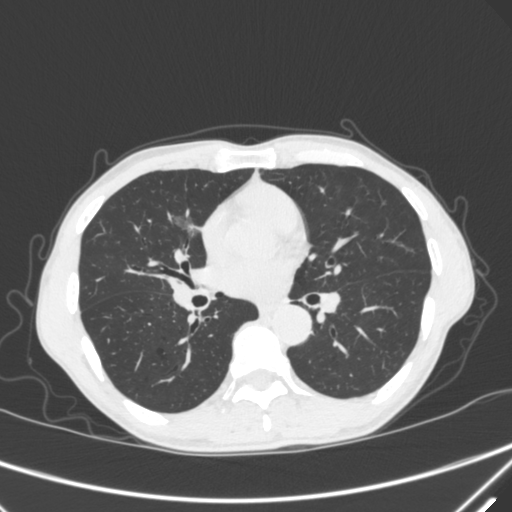
Chest CT, one axial slice; position 172 of 340 along the scan axis; 120 kVp; lung window (W 1500 / L -600 HU); 1 mm slice thickness; 512 × 512 image matrix. Male patient, age 67 years. From the clinical record (not read from this slice): clinical TNM (as recorded): T1c N0 M0; histopathological grade: G1-2.
Annotated regions visible in this slice (bounding box drawn by a radiologist):
- lung tumour (recorded histology: adenocarcinoma): bounding box <166,206,203,248> (left, top, right, bottom; pixels)